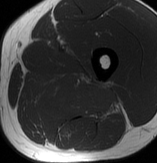
MRI of an extremity soft-tissue mass, one axial slice. Slice 42 of 70 in the series (ordered by position). MR volume resampled by the dataset authors to the PET/CT grid (not the native acquisition matrix). 3.27 mm slice thickness. 157 × 163 image matrix, field of view 153 × 159 mm. Male patient. From the clinical record (not read from this slice): histological type: extraskeletal osteosarcoma; grade: high; site of the primary tumour: left adductur.
Annotated regions visible in this slice (expert contour drawn on MRI and transferred to this co-registered scan by the dataset authors):
- gross tumour volume (mass): box from (x=24, y=72) to (x=123, y=123) px